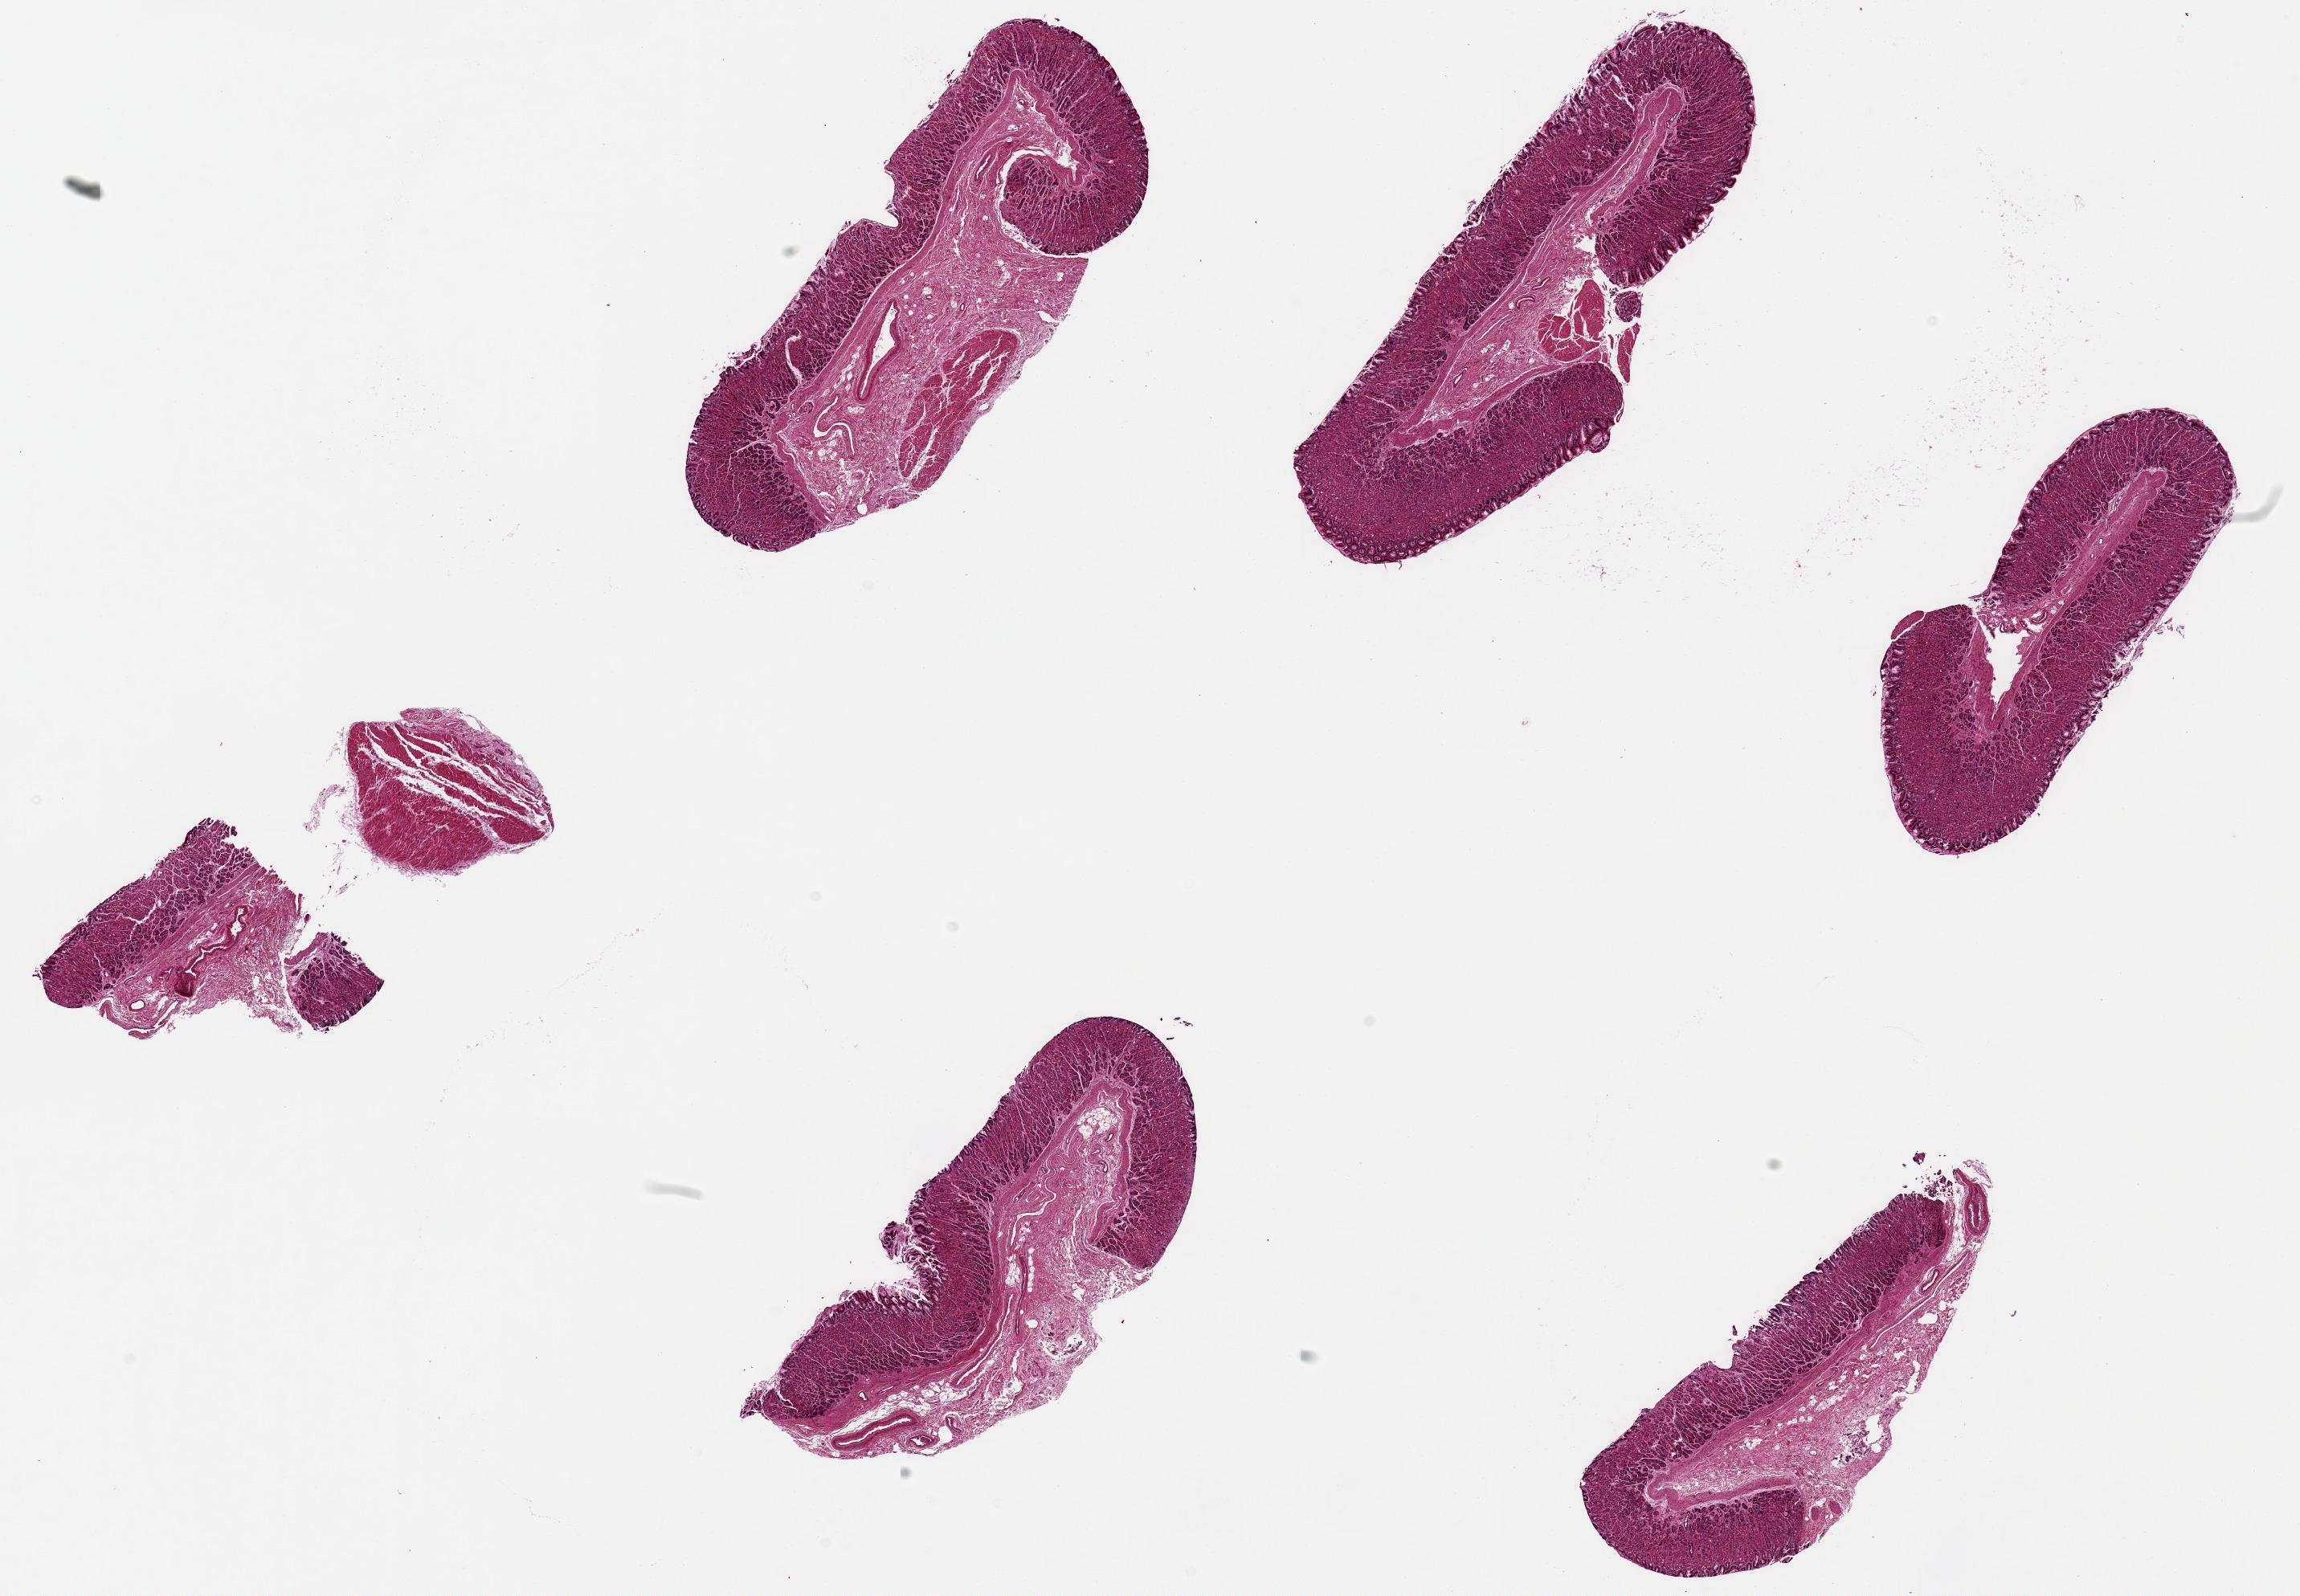
Hematoxylin and eosin (H&E) whole-slide image — low-resolution overview of the scanned area, about 22.6 x 15.7 mm (acquisition: 20x scan), PAXgene-fixed paraffin-embedded (PFPE) section, target tissue: stomach, donor tissue sample. Donor: female.
* review note (as recorded): 6 pieces, up to 6x2mm; extremely well preserved mucsoa, 30-90% of thickness